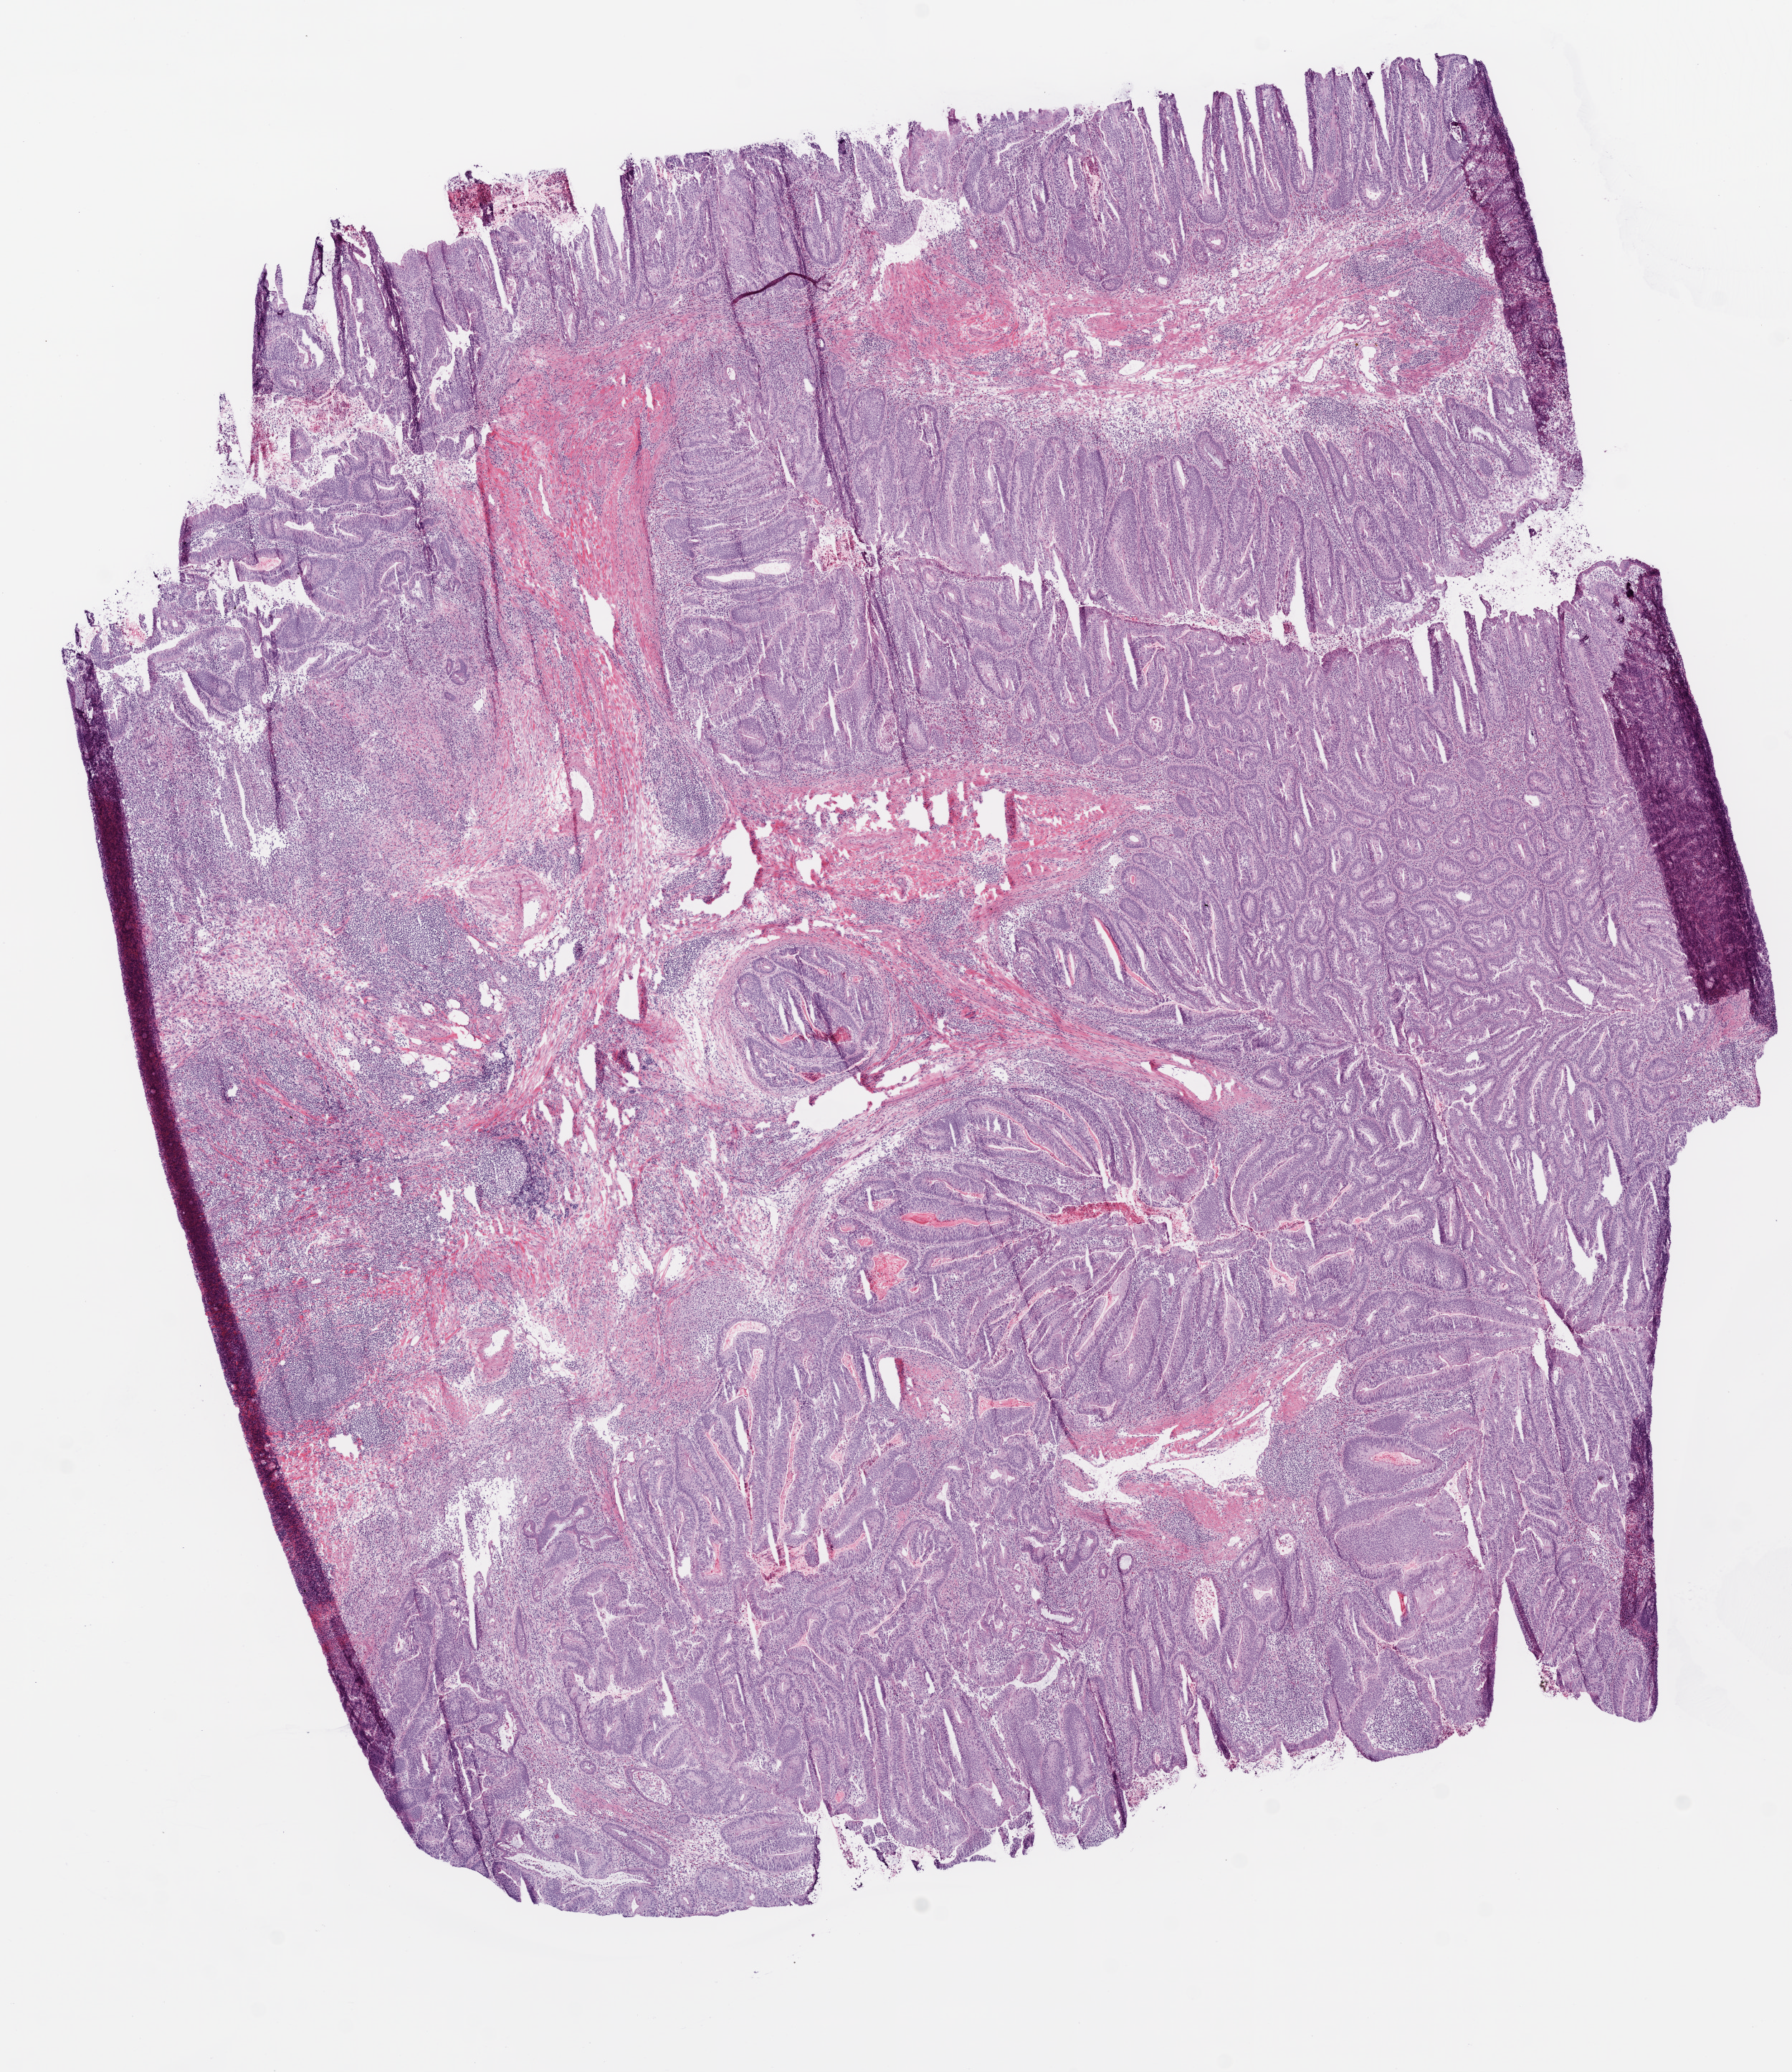
Digitized H&E-stained tissue section (whole slide) — whole scanned area (about 10.0 x 11.6 mm) shown as a low-resolution overview. Frozen section. Sample: primary tumour, colon. Male, age 73 years at initial diagnosis. Slide review estimates, as recorded: tumour cells 72%, tumour nuclei 83%, normal cells 20%, stromal cells 3%, necrosis 0%.
- AJCC pathologic stage: I
- TNM: T2 N0 M0
- pathologic diagnosis: Adenocarcinoma, NOS